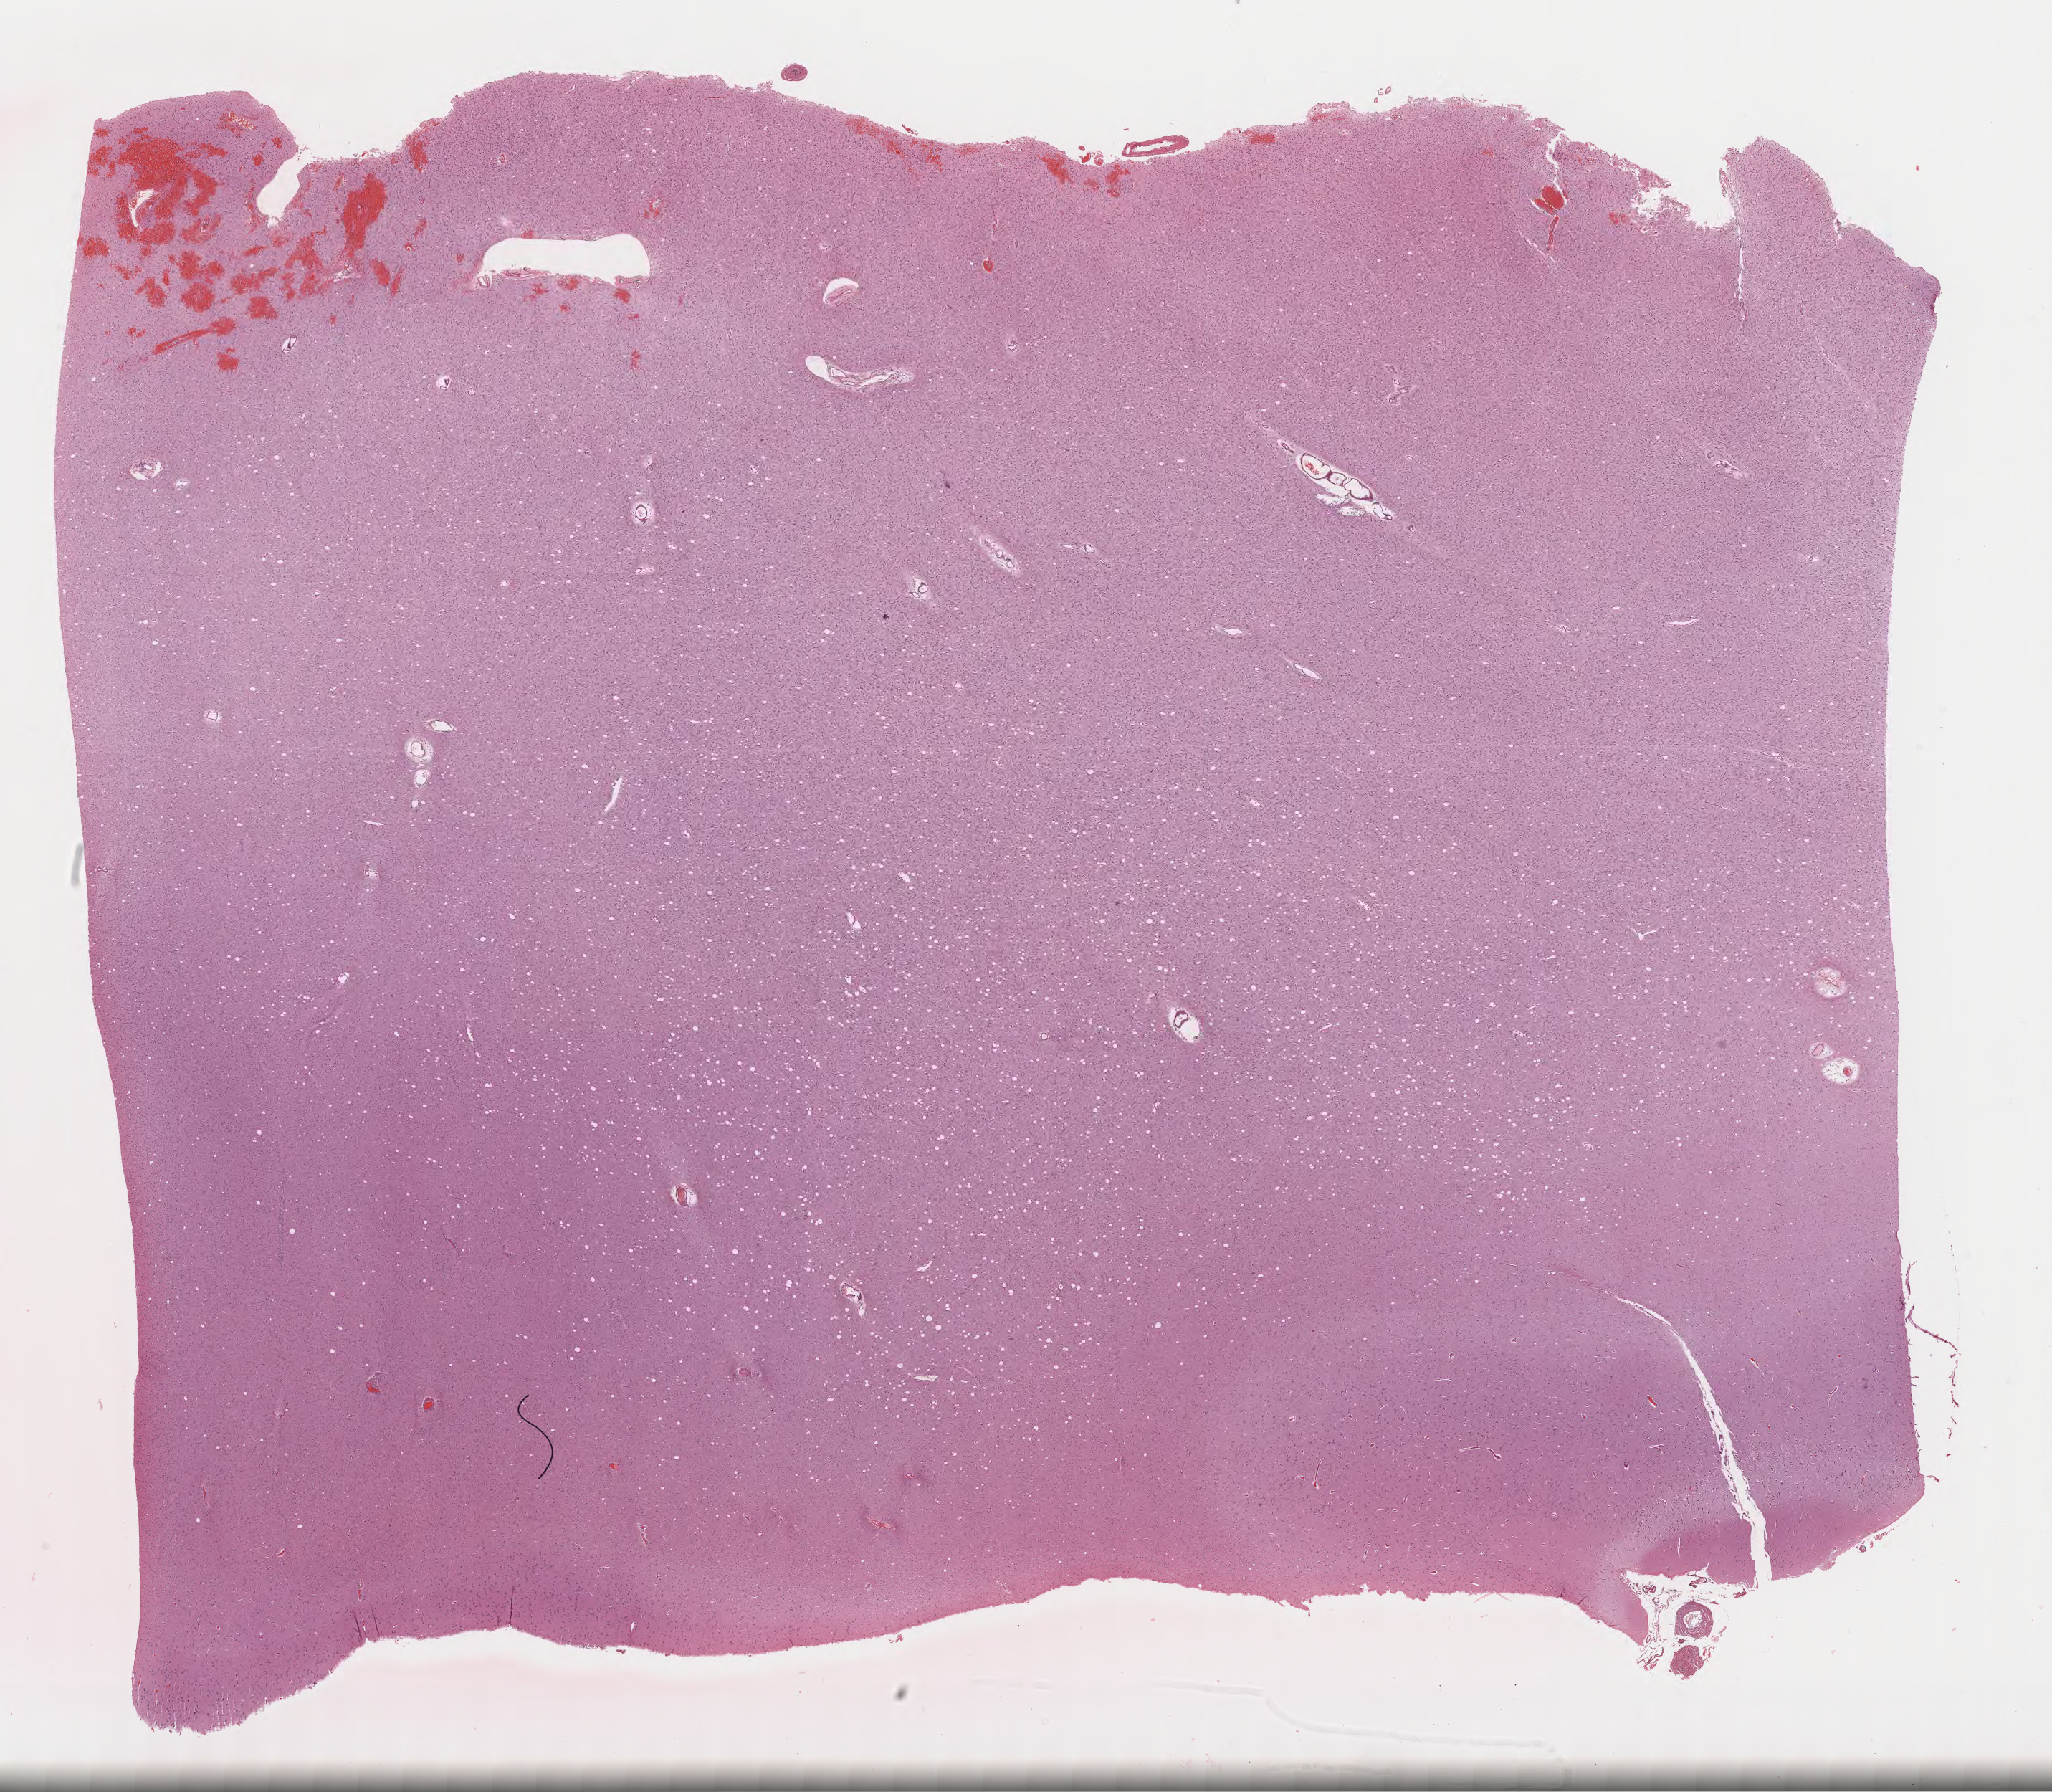
Haematoxylin and eosin whole-slide image of tumor tissue from the brain — whole scanned area (about 23.2 x 20.2 mm) shown as a low-resolution overview; FFPE section. Patient: female, age 205 months (17 years 1 month).
Recorded diagnosis: Astrocytoma, NOS.